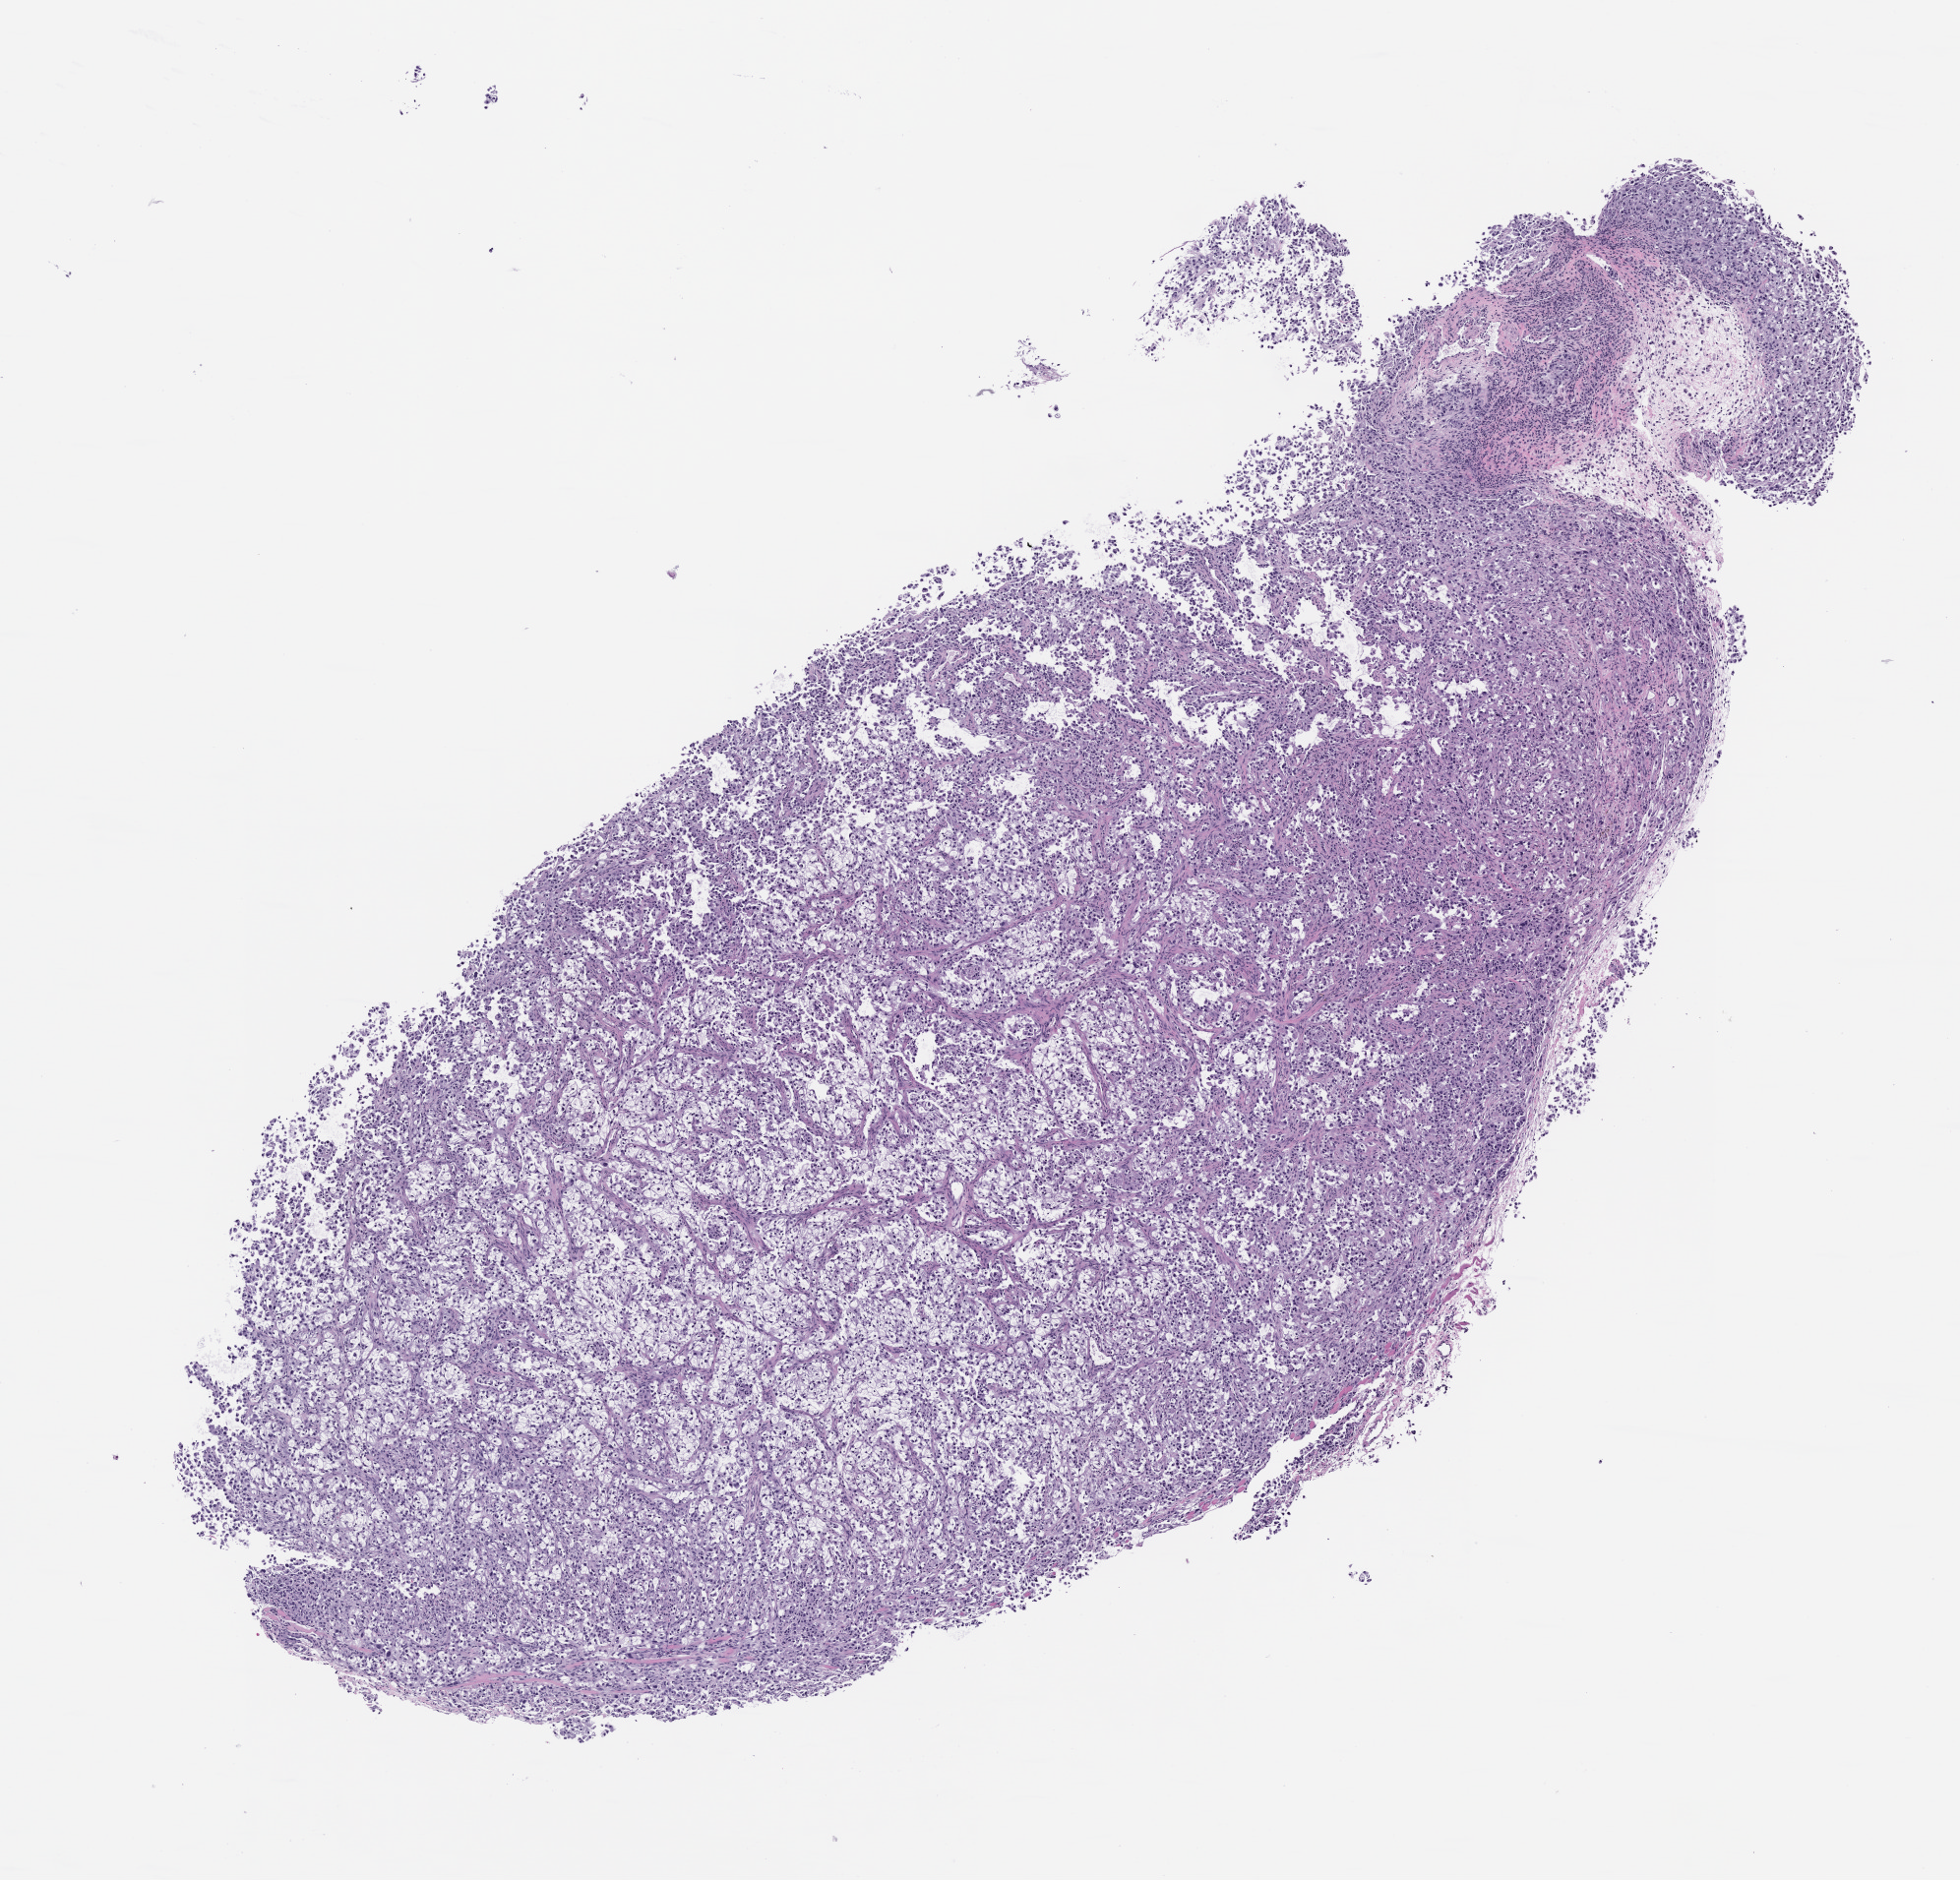
Whole-slide image, hematoxylin and eosin (H&E): patient-derived xenograft (human tumor grown in a mouse), passage 2 — low-resolution overview of the scanned area, about 8.0 x 7.7 mm. FFPE section. Originating tumor site category: genitourinary tract.
Originating patient diagnosis: Renal Cell Carcinoma, Not Otherwise Specified.